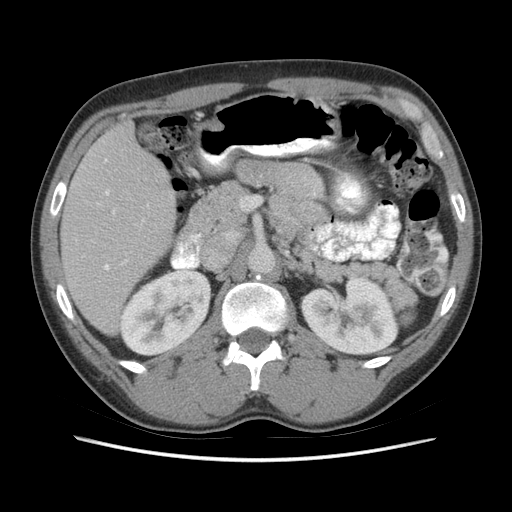
Contrast-enhanced abdominal CT (liver protocol), one axial slice; reconstruction kernel STANDARD; 140 kVp; soft-tissue window (W 400 / L 40 HU); 512 × 512 image matrix. Case-level facts recorded for this patient, not image findings: diagnosis: hepatocellular carcinoma (patient treated with transarterial chemoembolisation; whether this scan precedes or follows treatment is not stated here); TNM stage (as recorded): Stage-IIIA; Child-Pugh class: A; tumour nodularity: multinodular; tumour size: 6.6 cm.
Outlined on this slice (semi-automatically segmented with operator editing):
- liver parenchyma outside the tumour (the mass and vessels are separate outlines, so this box may not span the whole liver): bounding box (x1, y1, x2, y2) in pixels: (60, 124, 176, 334)
- liver vessels: (104, 160, 127, 270)